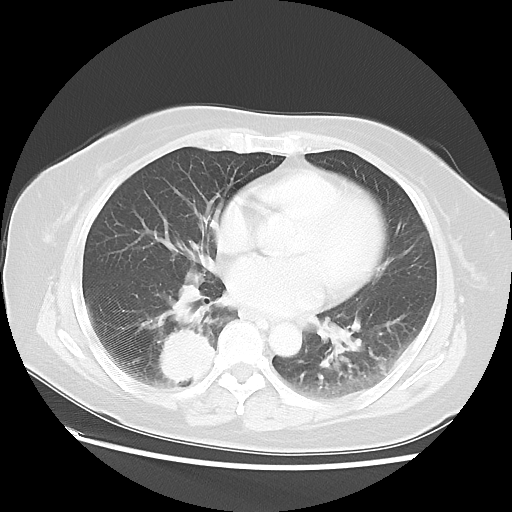
Chest CT, one axial slice. Reconstruction kernel LUNG. Lung window (W 1500 / L -600 HU). 5 mm slice thickness. 512 × 512 image matrix. Patient: female, 69 years. From the clinical record (not read from this slice): clinical TNM (as recorded): T2 N1 M1a.
Outlined on this slice (rectangle marked by the reading radiologist):
- lung tumour (recorded histology: adenocarcinoma): bounding box (x1, y1, x2, y2) in pixels: (151, 322, 217, 386)